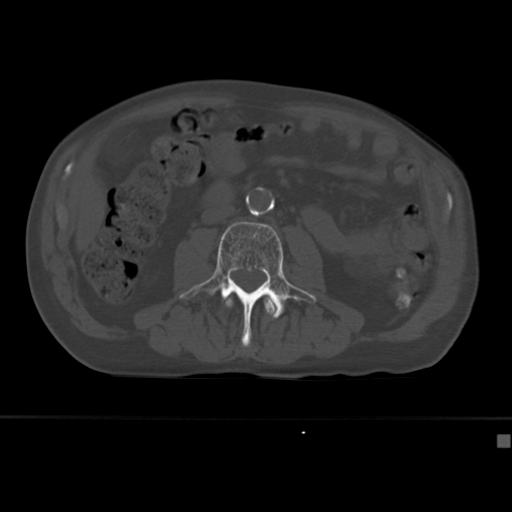
CT including the spine, one axial slice. Position 130 of 430 along the scan axis. Reconstruction kernel Br40s. 120 kVp. Bone window (W 1800 / L 400 HU). 1.5 mm slice thickness. 512 × 512 image matrix, field of view 337 × 337 mm. Patient: male, 64 years. Case-level facts recorded for this patient, not image findings: primary cancer: uterus; vertebrae with lytic lesions (as recorded): T1, T4, T5, T7, L5.
Structures marked on this image (semi-automatic segmentation, software-assisted and operator-edited):
- L2 vertebra: bounding box [x1, y1, x2, y2] px = [223, 297, 277, 316]
- L3 vertebra: [179, 222, 317, 347]